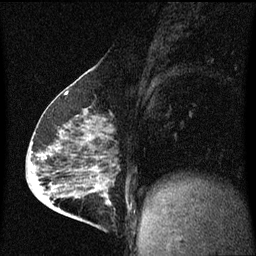
Breast MRI (dynamic contrast-enhanced), one sagittal slice. Dynamic contrast-enhanced series, image 2 of 3 at this slice position (ordered by acquisition). 1.5 T. TE 4.2 ms, TR 8 ms. 2 mm slice thickness. 256 × 256 image matrix, field of view 200 × 200 mm. Female patient, age 63 years.
Outlined on this slice (semi-automatically segmented with operator editing):
- analysis volume of interest (the breast-tissue region the enhancement analysis was run in; not a lesion): box from (x=88, y=182) to (x=117, y=229) px
- tumour enhancement mask (voxels above the 70 % enhancement threshold inside the analysis volume of interest): (x=90, y=190)–(x=109, y=203)